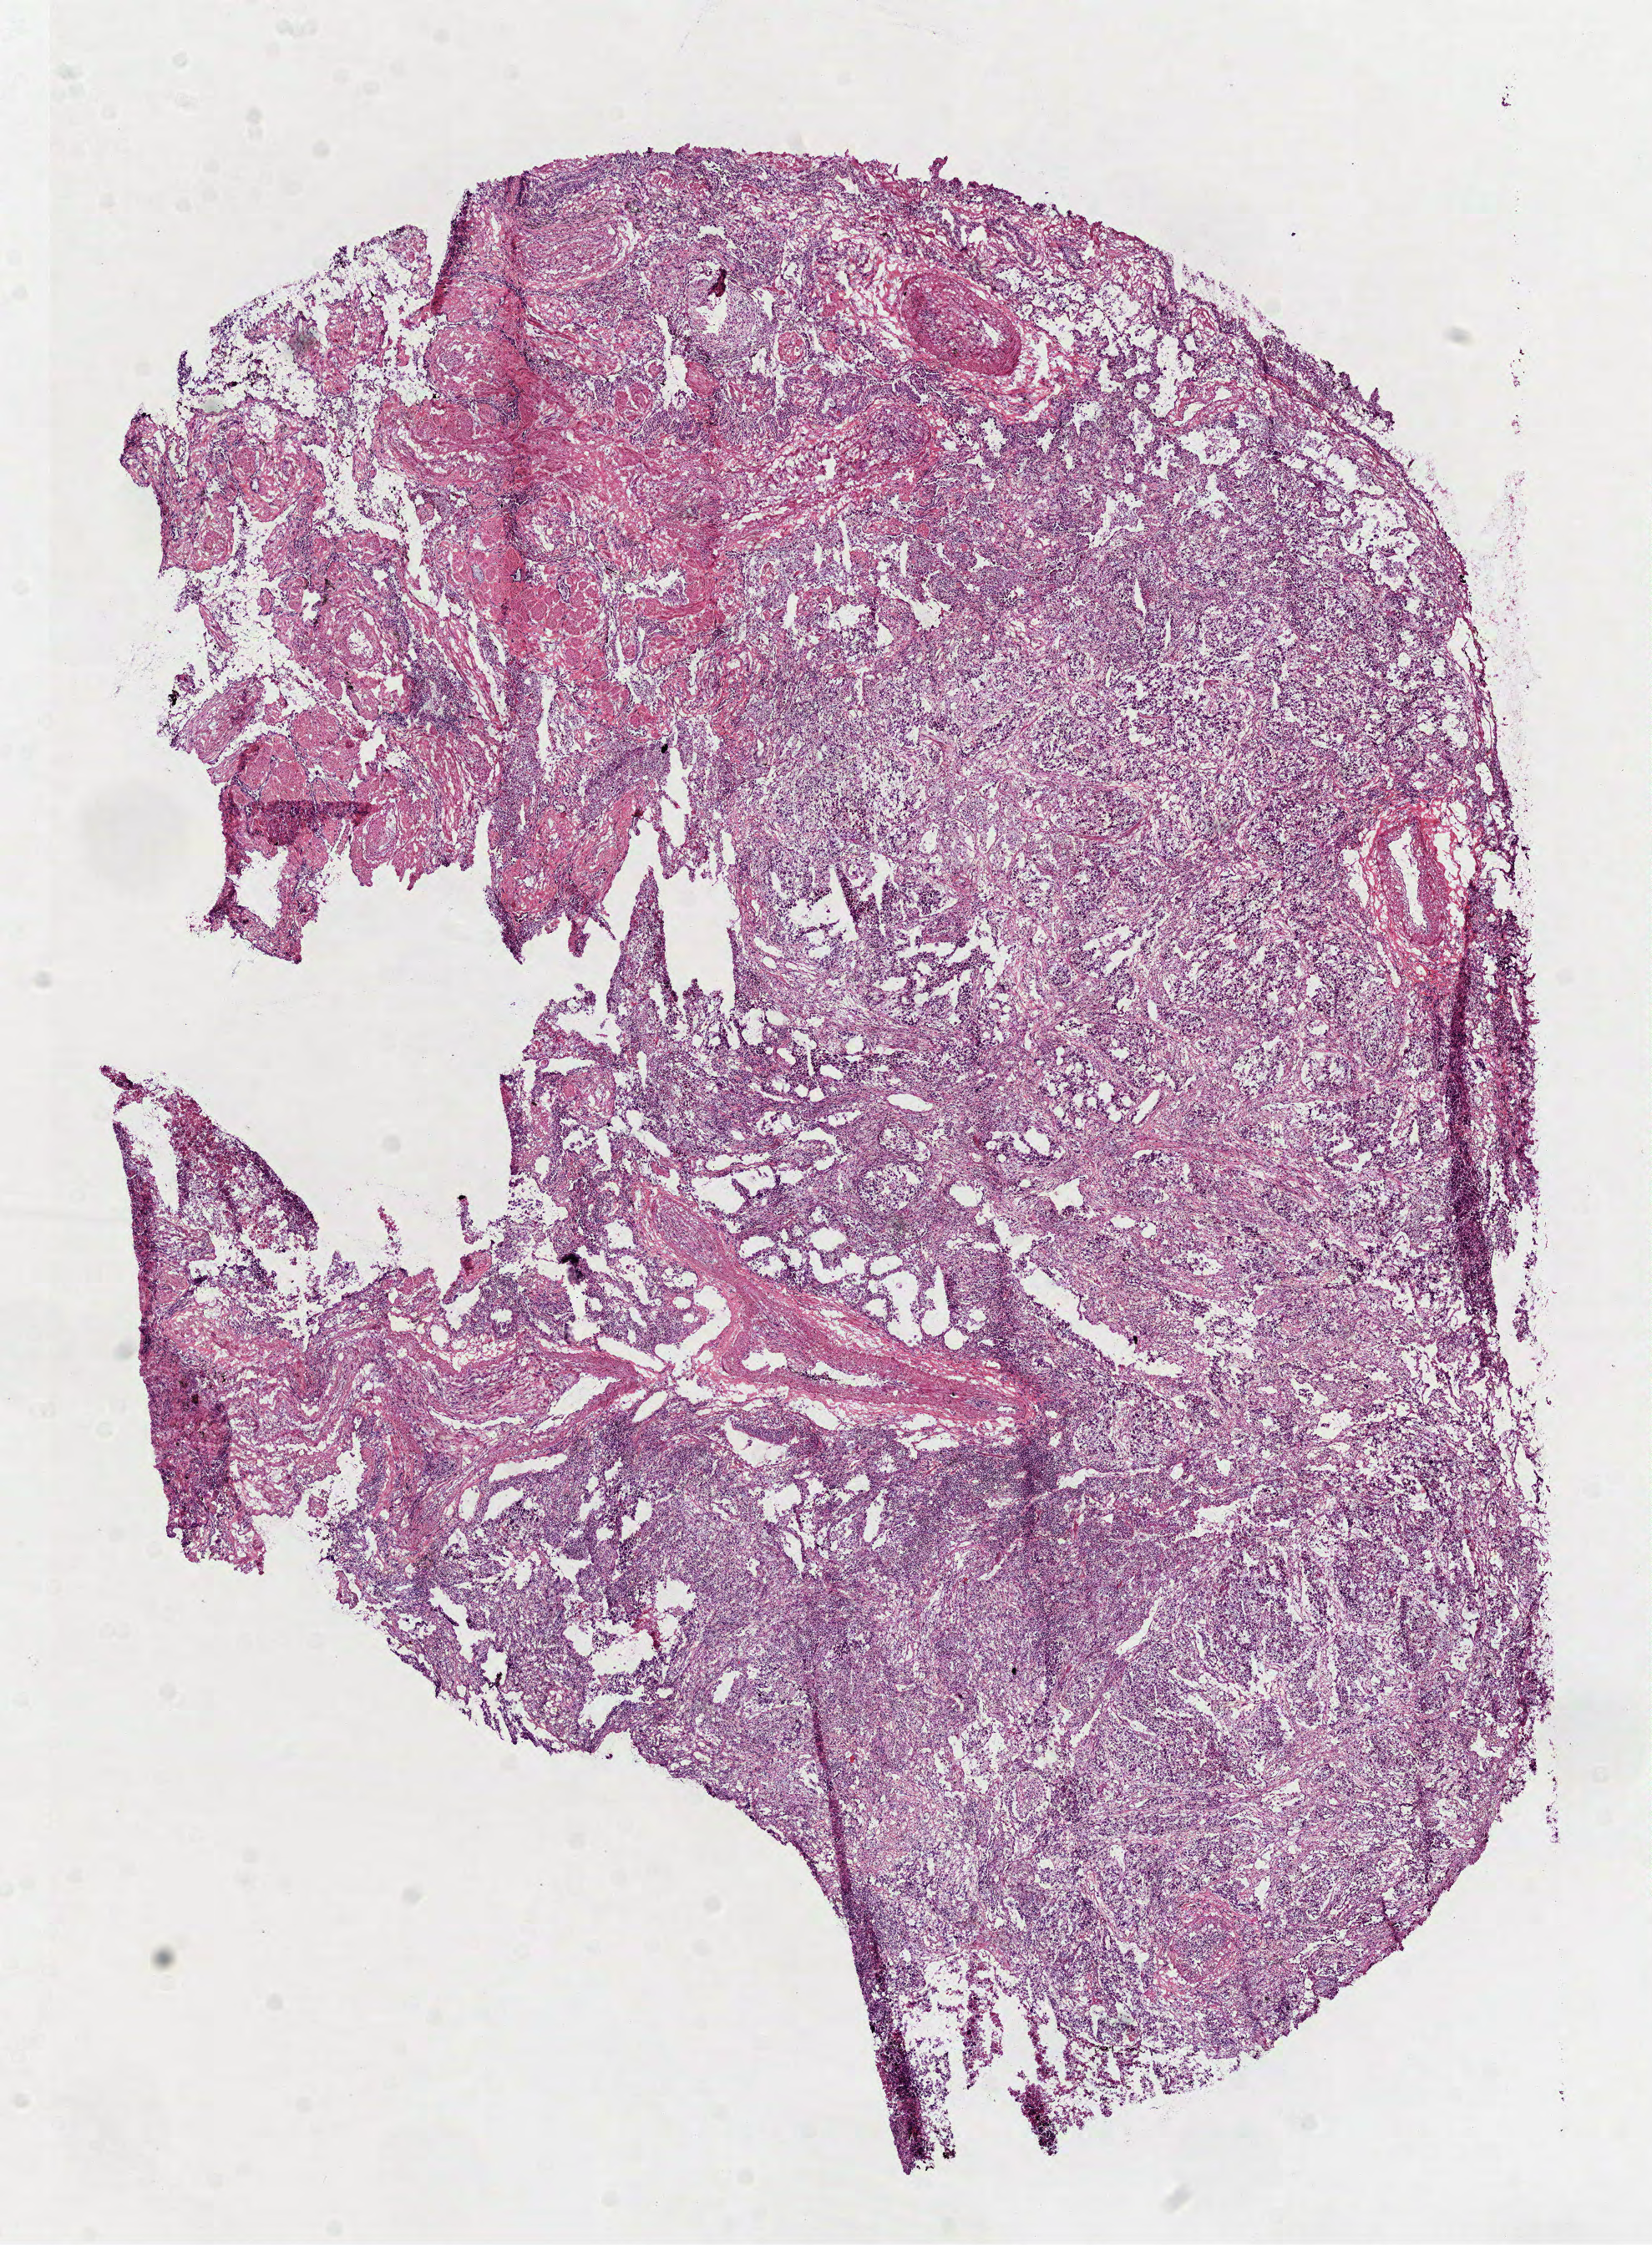
Whole-slide histology image, H&E-stained, shown as a low-resolution overview of the whole scanned area (about 8.0 x 10.8 mm, acquisition: 40x scan). Frozen section from the top of the tissue portion. Sample: primary tumour, lung. Male, age 67 years at initial diagnosis. Pathologist review of this section (percent, as recorded): tumour cells 85%, tumour nuclei 70%, normal cells 0%, stromal cells 15%, necrosis 0%.
AJCC pathologic stage: IIA (7th edition). Laterality: right. Diagnosis: Squamous cell carcinoma, NOS (upper lobe, lung).